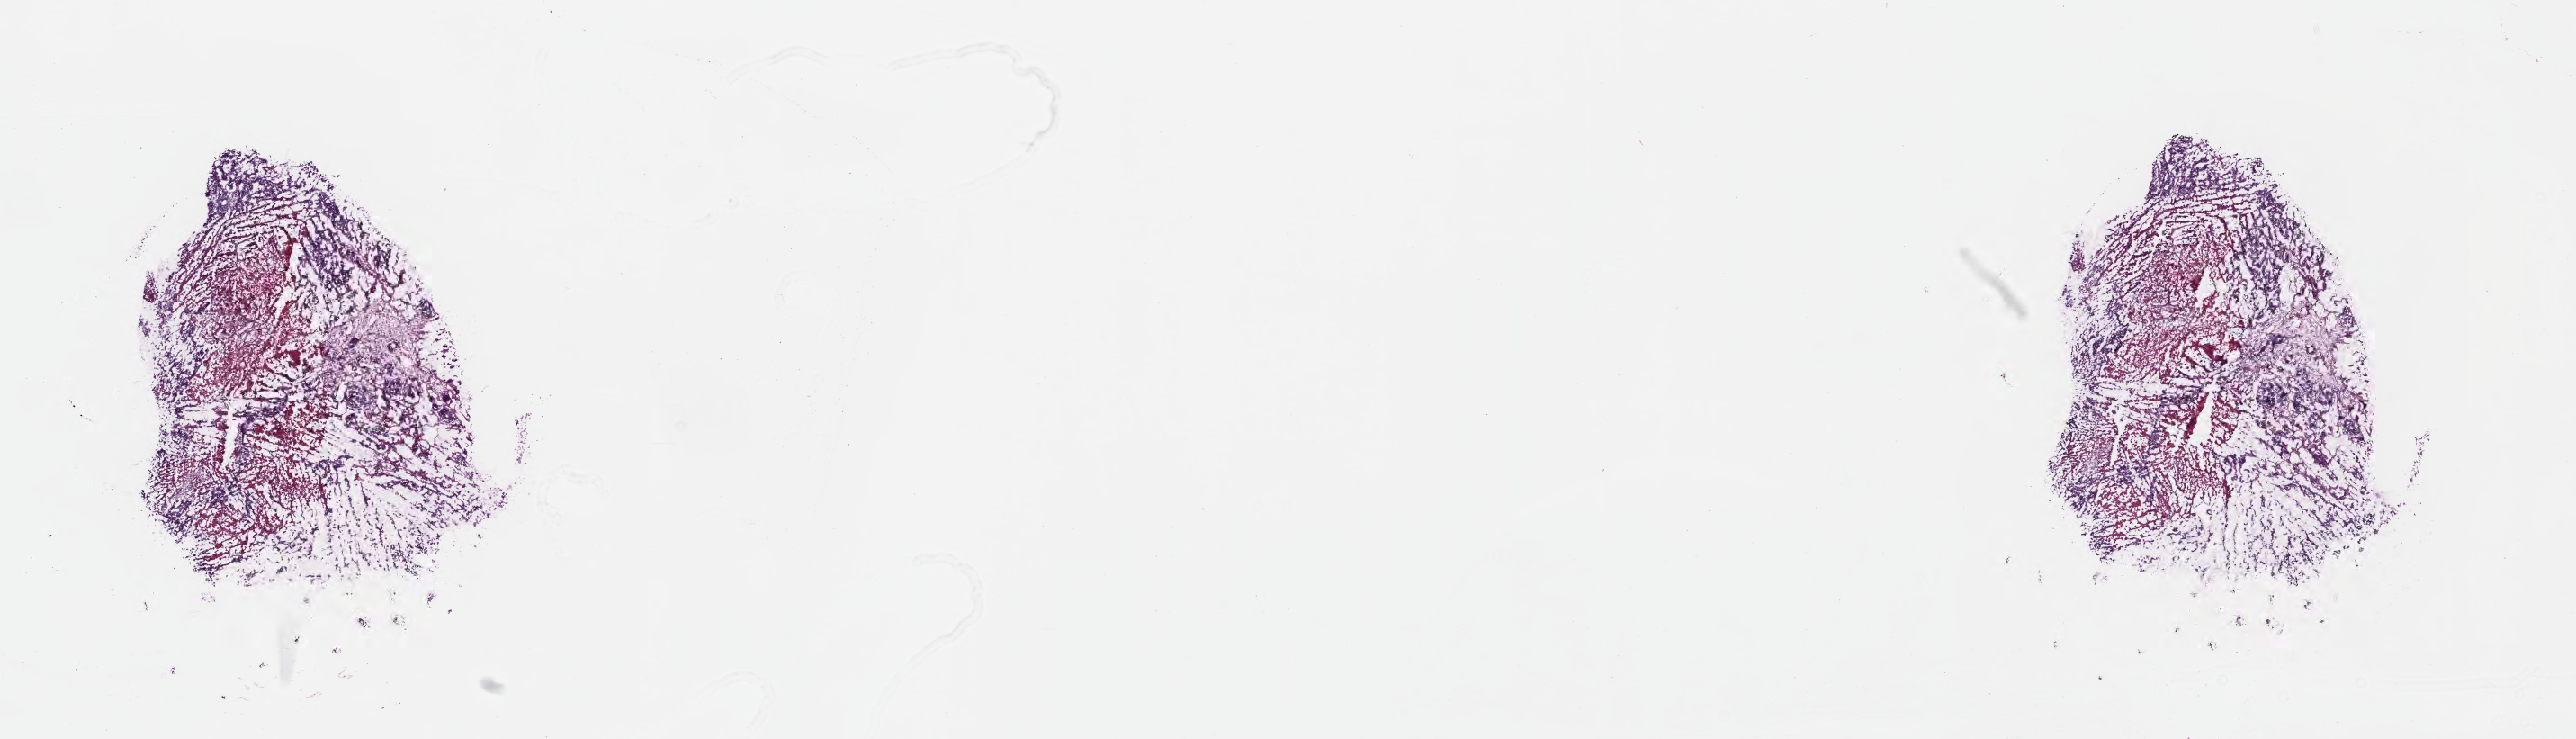
Whole-slide image, haematoxylin and eosin stain — low-resolution overview of the scanned area, about 23.1 x 6.6 mm. Frozen section. Specimen: metastatic tumor tissue, resected from liver. Male patient; age at initial diagnosis 46 years. Slide review estimates, as recorded: tumor cells 40%, tumor nuclei 60%.
Patient diagnosis (primary): Adenocarcinoma, NOS.